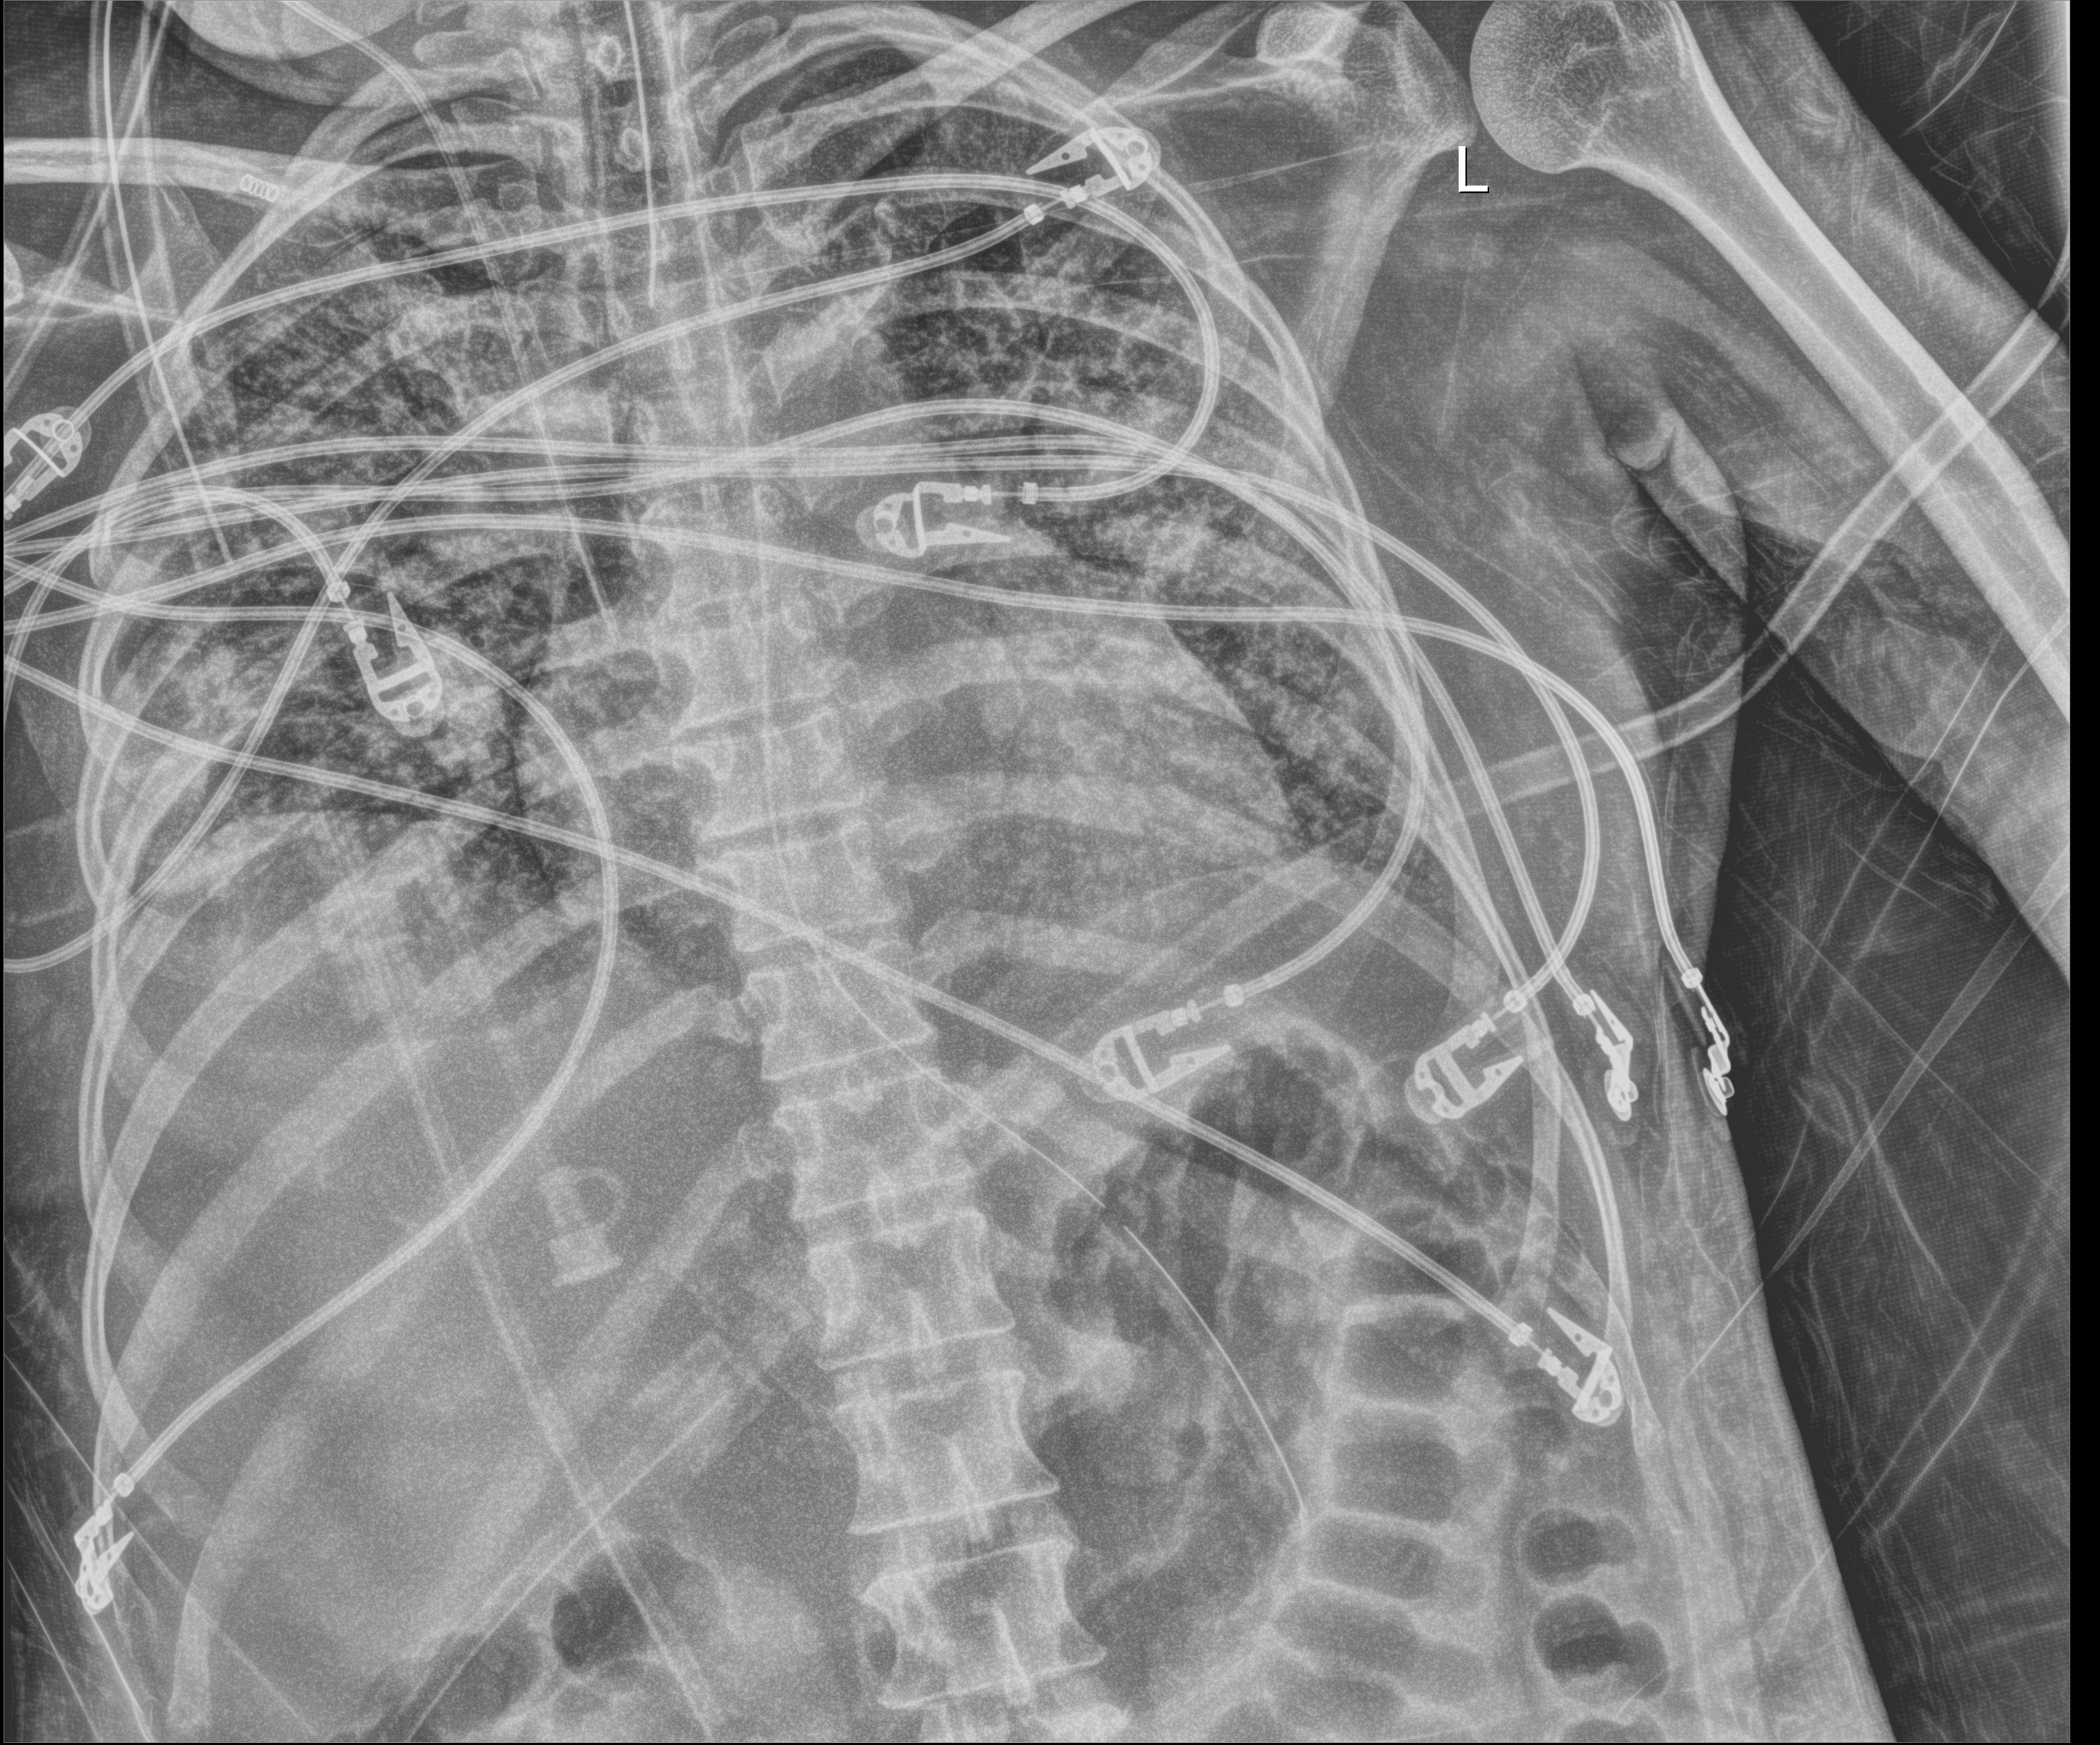
Bedside chest radiograph (digital radiography). Female patient hospitalised with COVID-19, age 18–59 years.
From the hospital-stay record, not from the radiograph (when in the stay this image was taken is not recorded):
- admitted to intensive care during this hospital stay: yes
- other chronic lung disease (admission record): no